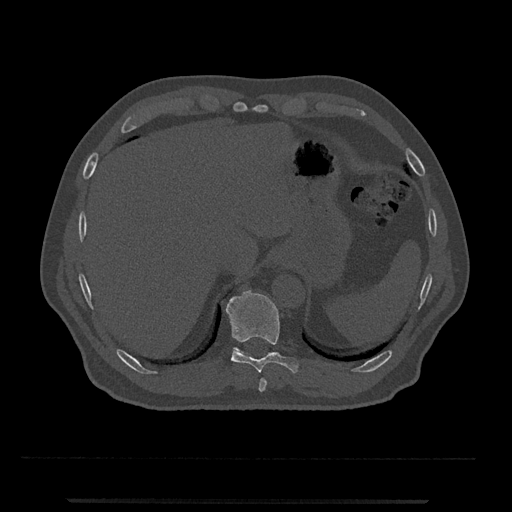
CT including the spine, one axial slice. Slice 513 of 797 in the series (ordered by position). Reconstruction kernel Br40s/3. 120 kVp. Bone window (W 1800 / L 400 HU). 512 × 512 image matrix, field of view 419 × 419 mm. Male patient, age 63 years. From the clinical record (not read from this slice): primary cancer: prostate.
Structures marked on this image (semi-automatically segmented with operator editing):
- T10 vertebra: box from (x=225, y=290) to (x=299, y=374) px
- T11 vertebra: (x=233, y=347)–(x=246, y=355)
- T9 vertebra: (x=258, y=378)–(x=267, y=392)